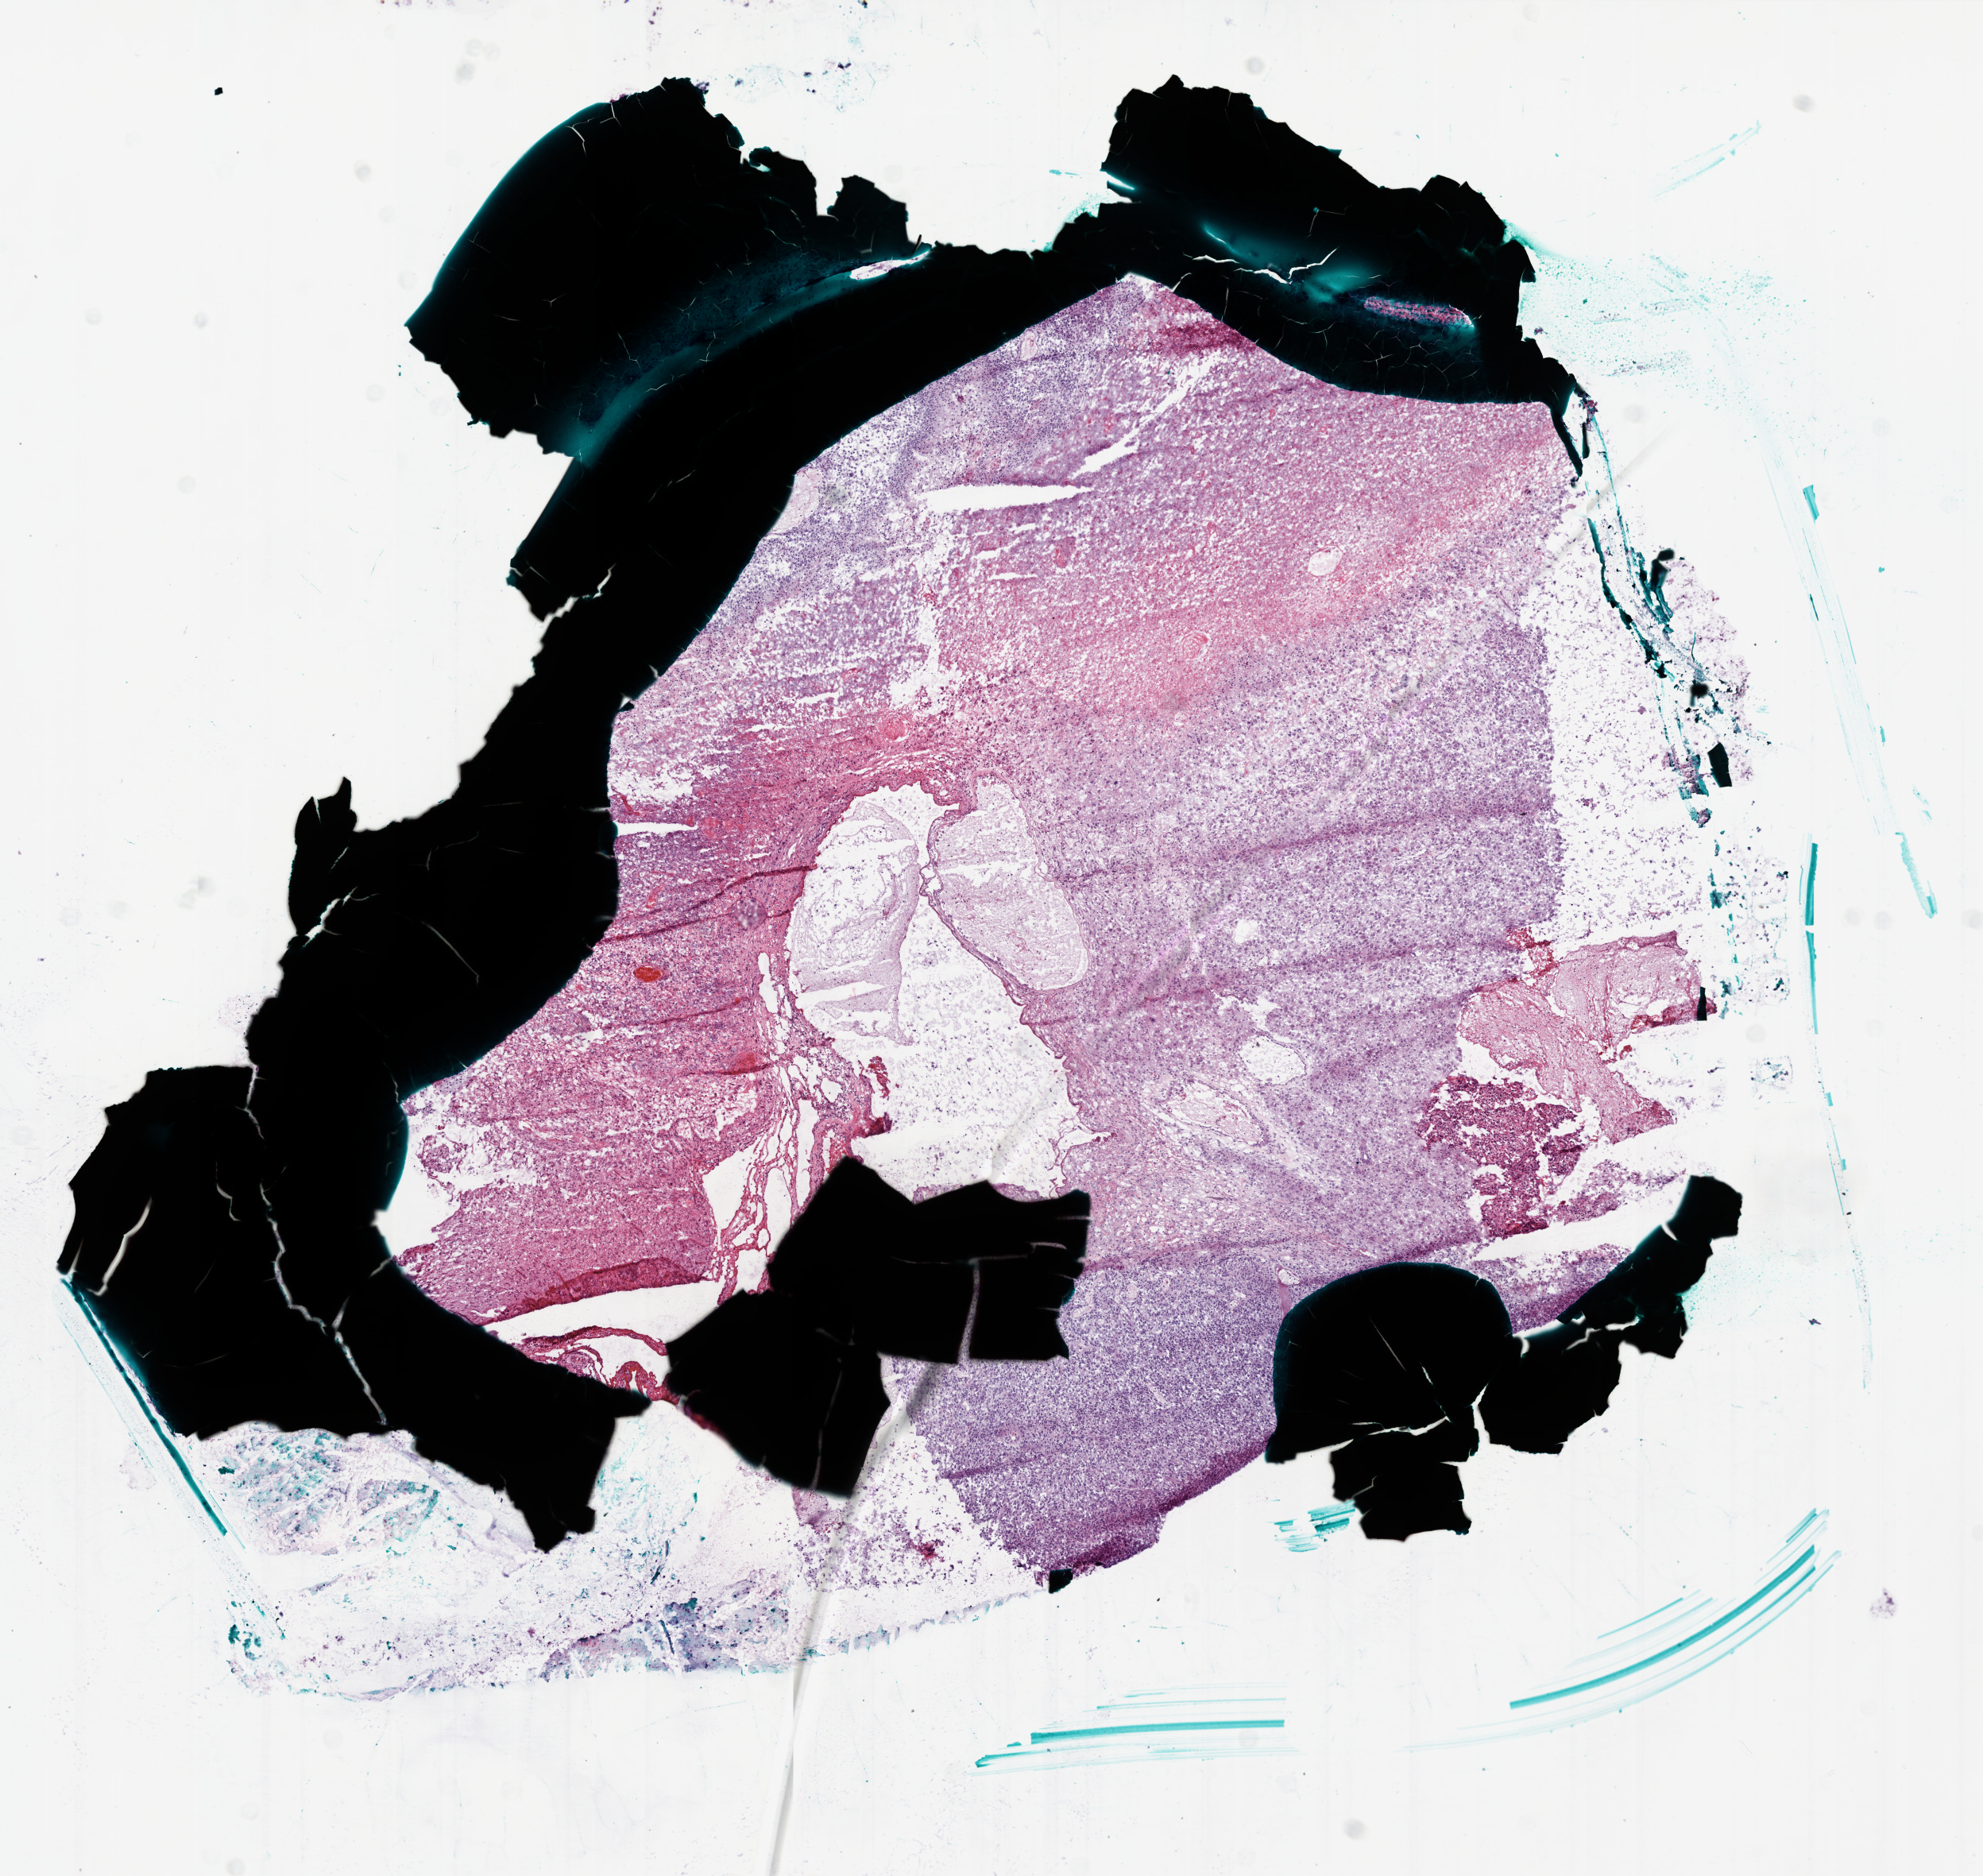
H&E whole-slide image — whole scanned area (about 10.0 x 9.4 mm, acquisition: 20x scan) shown as a low-resolution overview. Frozen section from the bottom of the tissue portion. Primary tumour sample from the brain. Male, age 54 years at initial diagnosis. Pathologist review of this section (percent, as recorded): tumour cells 50%, tumour nuclei 100%, normal cells 0%, stromal cells 0%, necrosis 50%.
Pathologic diagnosis: Glioblastoma.